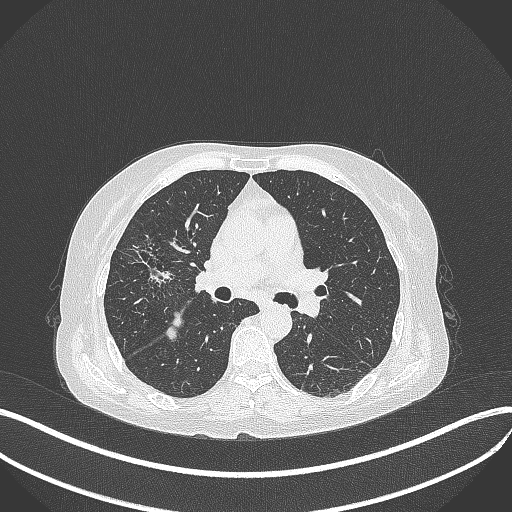
Chest CT, one axial slice; position 232 of 429 along the scan axis; reconstruction kernel B70f; 120 kVp; lung window (W 1500 / L -600 HU); 512 × 512 image matrix, field of view 400 × 400 mm. Patient: female, 69 years. Case-level facts recorded for this patient, not image findings: clinical TNM (as recorded): T1b N3 M0.
Outlined on this slice (bounding box drawn by a radiologist):
- lung tumour (recorded histology: small cell carcinoma): bounding box (x1, y1, x2, y2) in pixels: (125, 238, 179, 290)